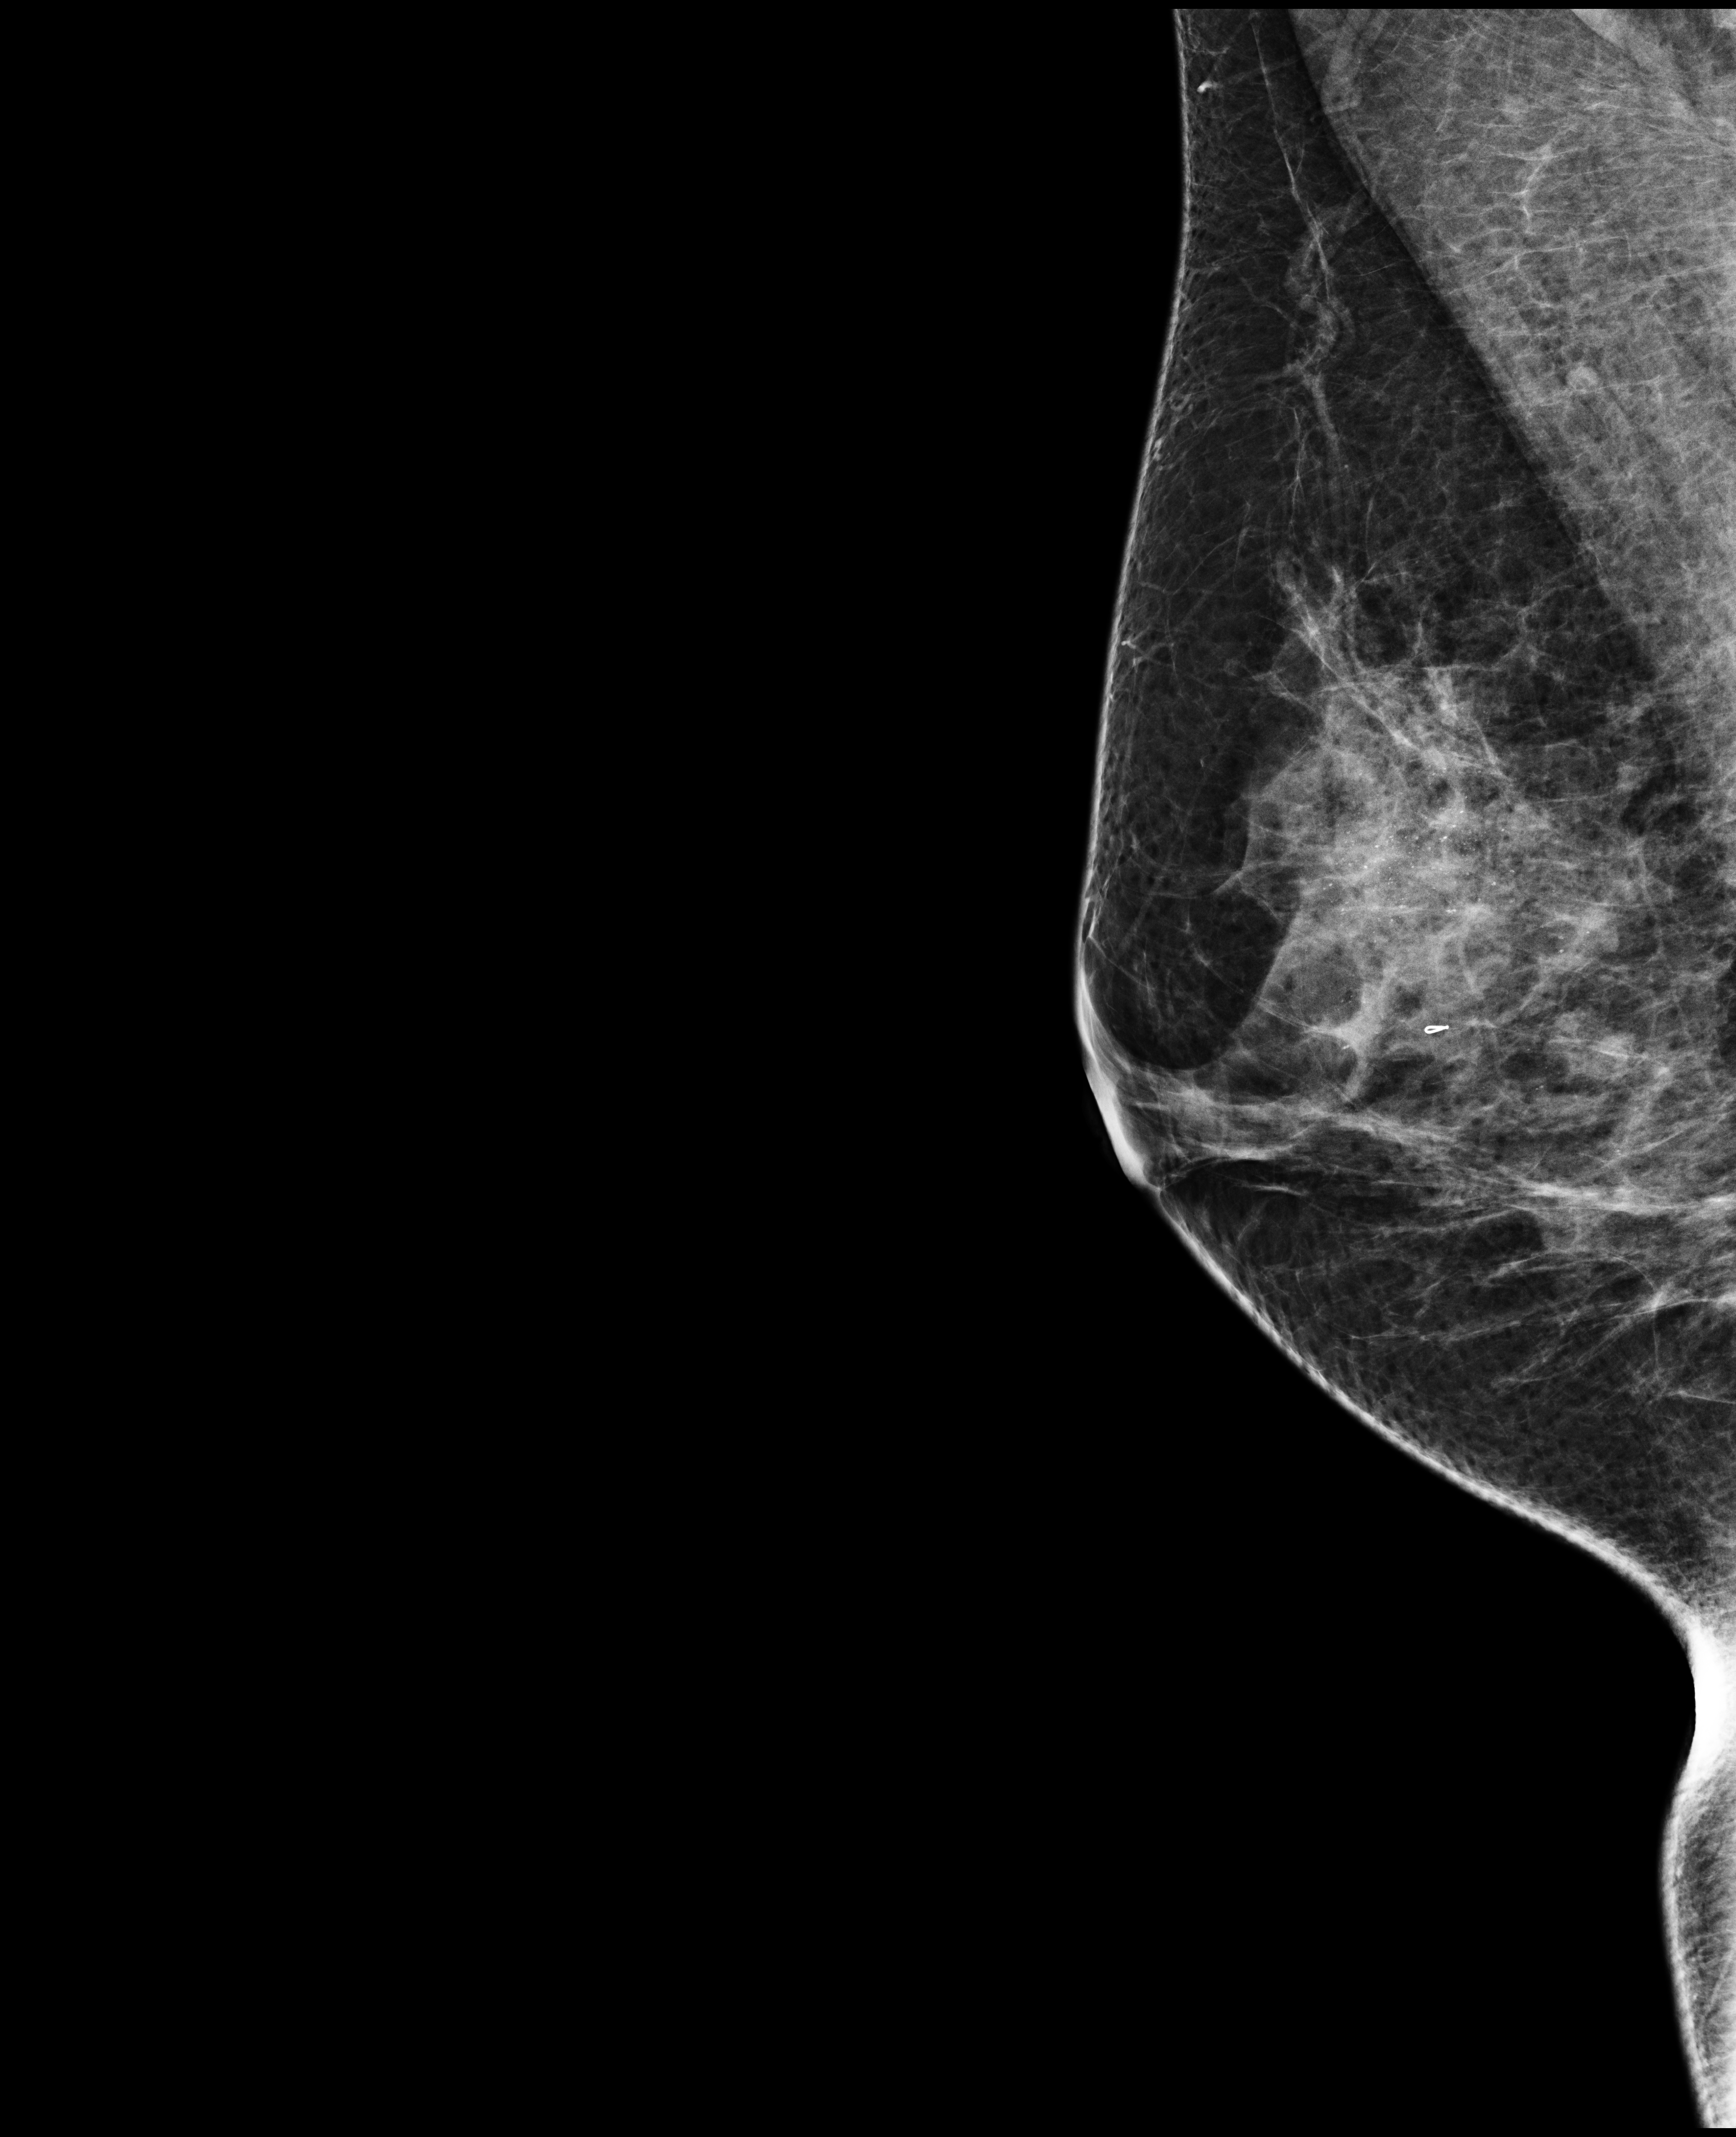
Screening examination. Patient aged 49 years (female).
Image type: full-field digital mammogram. Breast: right. Projection: mediolateral oblique (MLO) view.